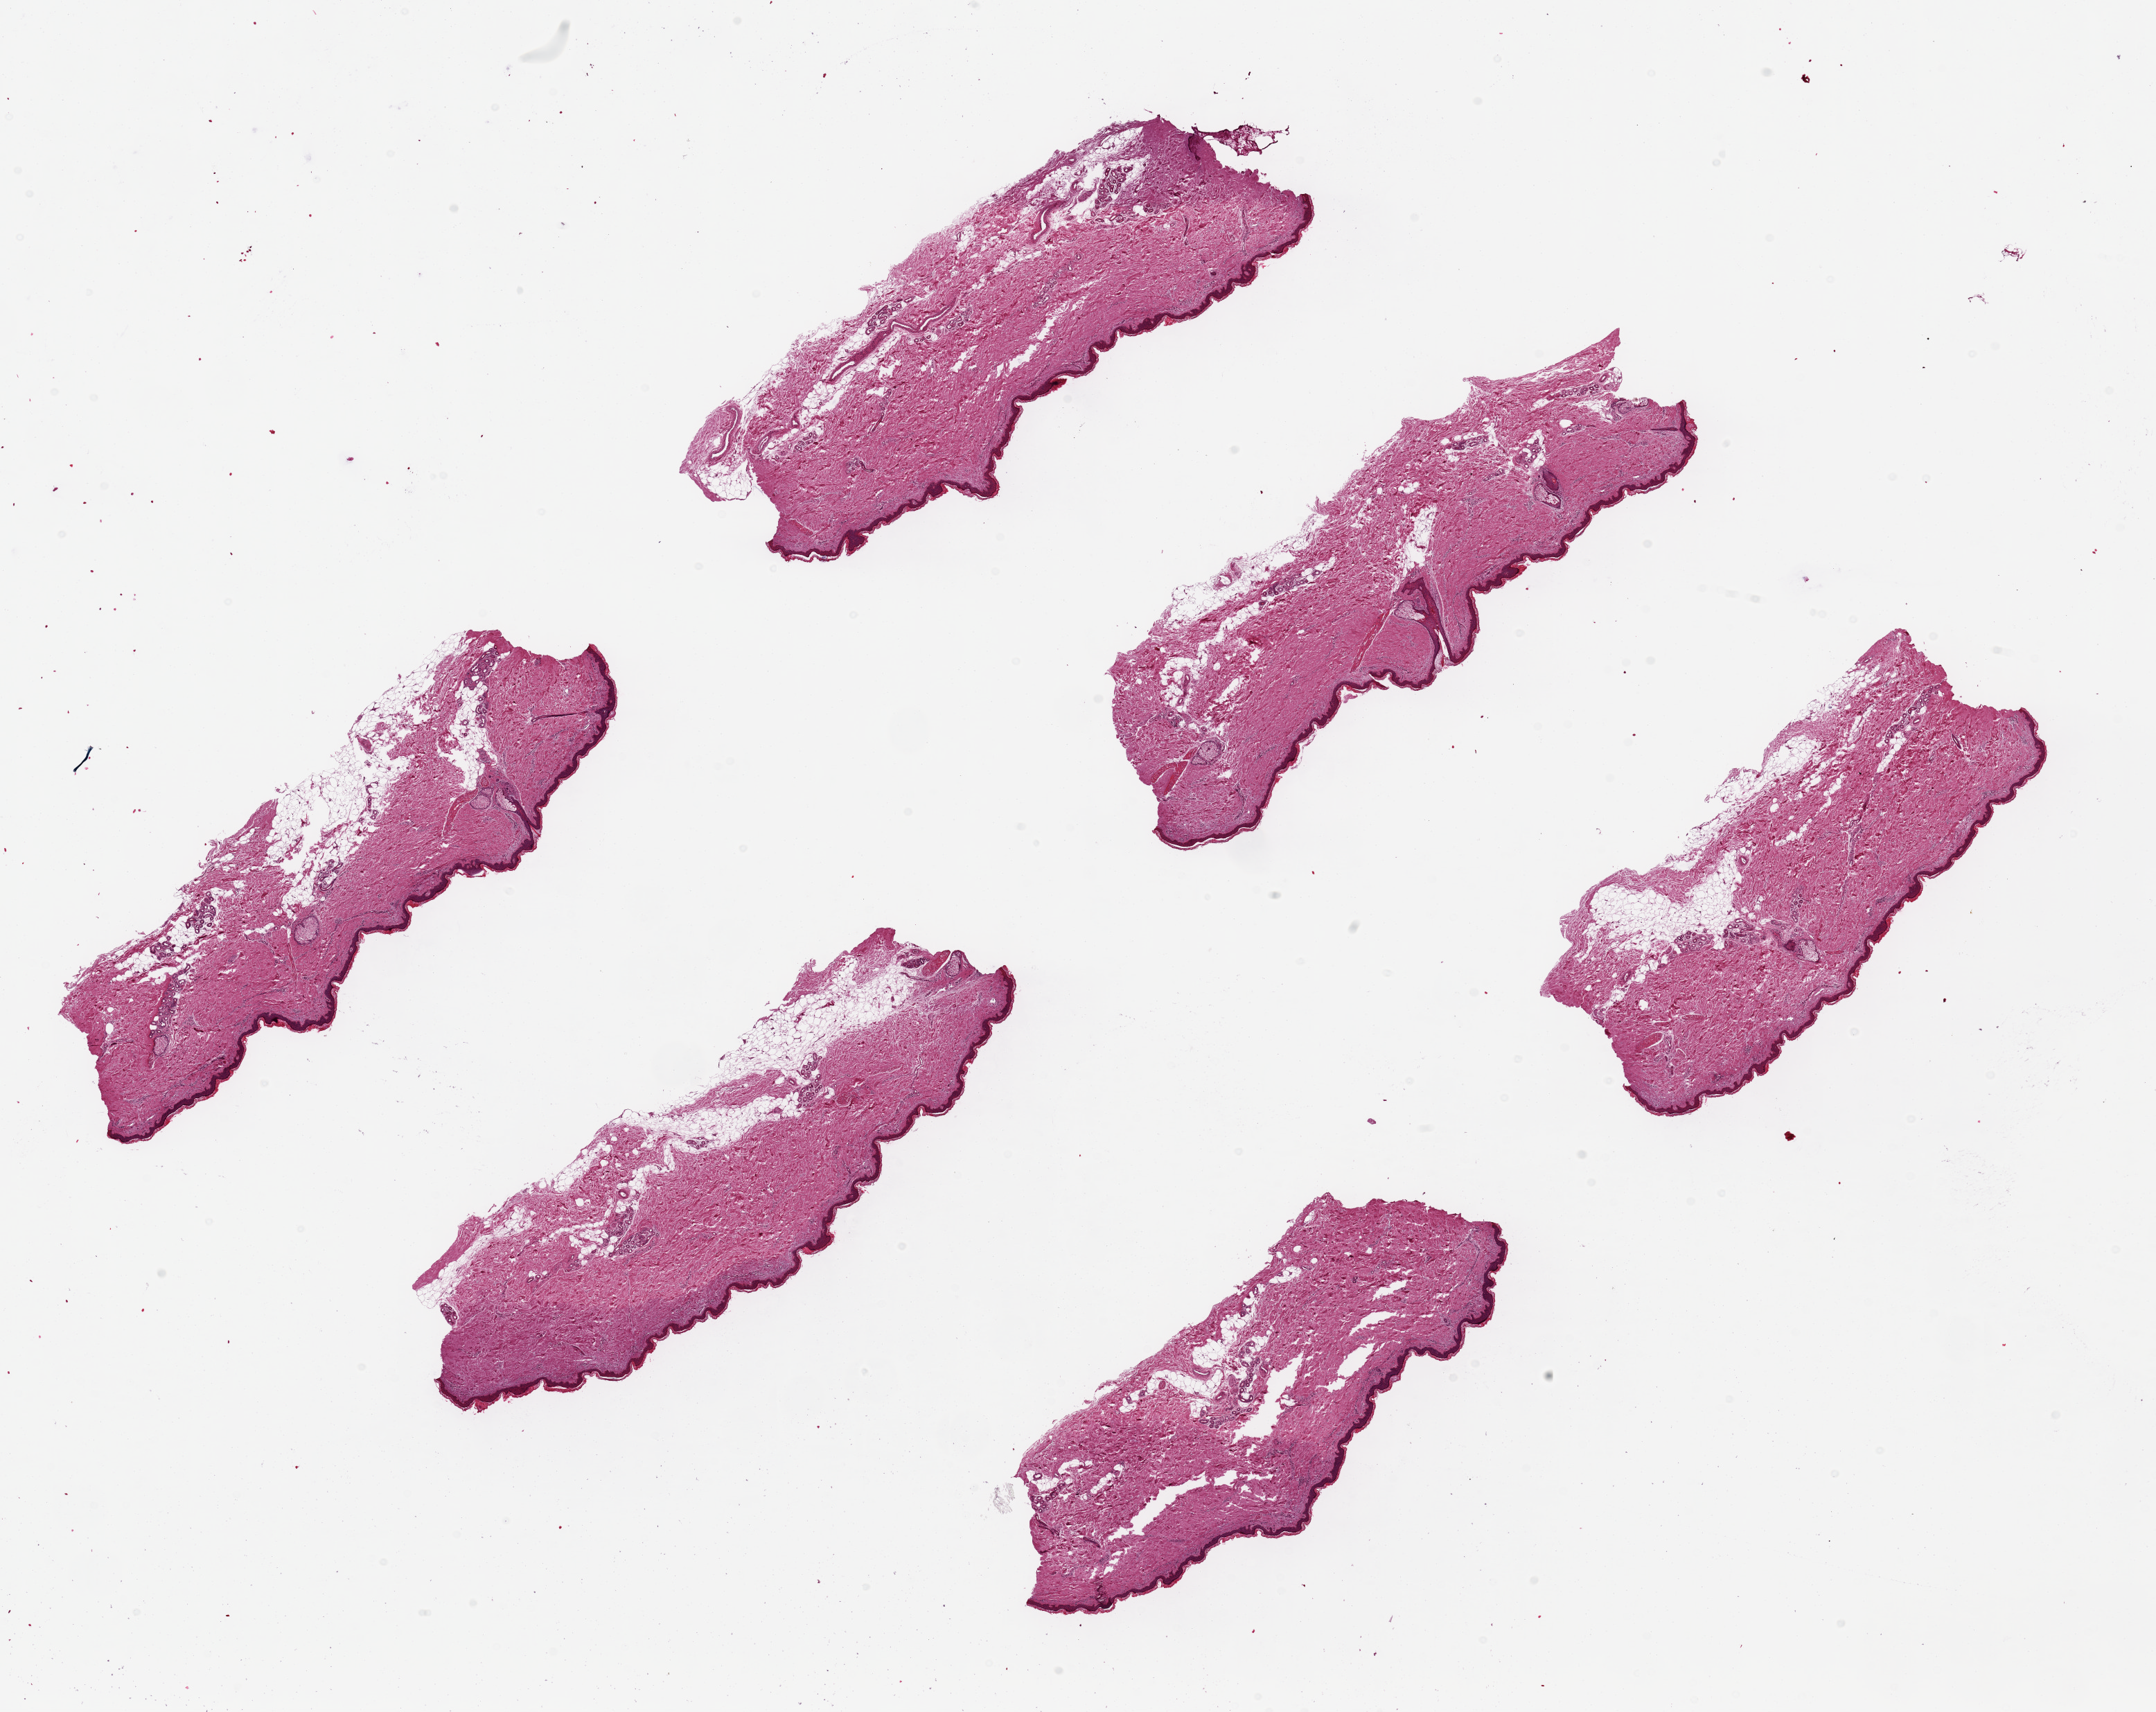
Whole-slide image, haematoxylin and eosin stain, a low-resolution overview of the entire scanned area, about 24.6 x 19.5 mm (from a 20x scan), PAXgene-fixed paraffin-embedded (PFPE) section, section of skin of lower leg (target tissue), donor tissue sample. Male donor.
* review note (as recorded): 6 pieces ~6.5x2.5mm. Squamous epithelium is ~1-3% of thickness